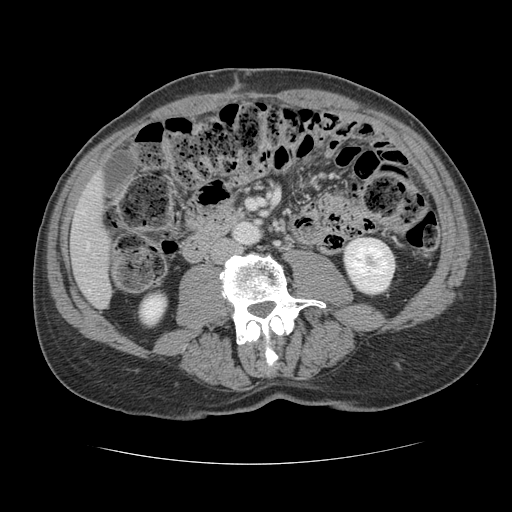
Contrast-enhanced abdominal CT, one axial slice; position 32 of 134 along the scan axis; reconstruction kernel STANDARD; intravenous contrast given; soft-tissue window (W 400 / L 40 HU); 2.5 mm slice thickness; 512 × 512 image matrix, field of view 377 × 377 mm. Male patient, age 68 years. From the clinical record (not read from this slice): diagnosis: colorectal cancer liver metastases, imaged before liver resection; multiple liver metastases: yes; largest metastasis: 2.2 cm; disease in both lobes: no.
Outlined on this slice (manually delineated by an expert):
- hepatic veins: bounding box <87,246,89,248> (left, top, right, bottom; pixels)
- liver: <72,178,111,308>
- planned liver remnant (the part of the liver to remain after resection): <72,178,111,308>